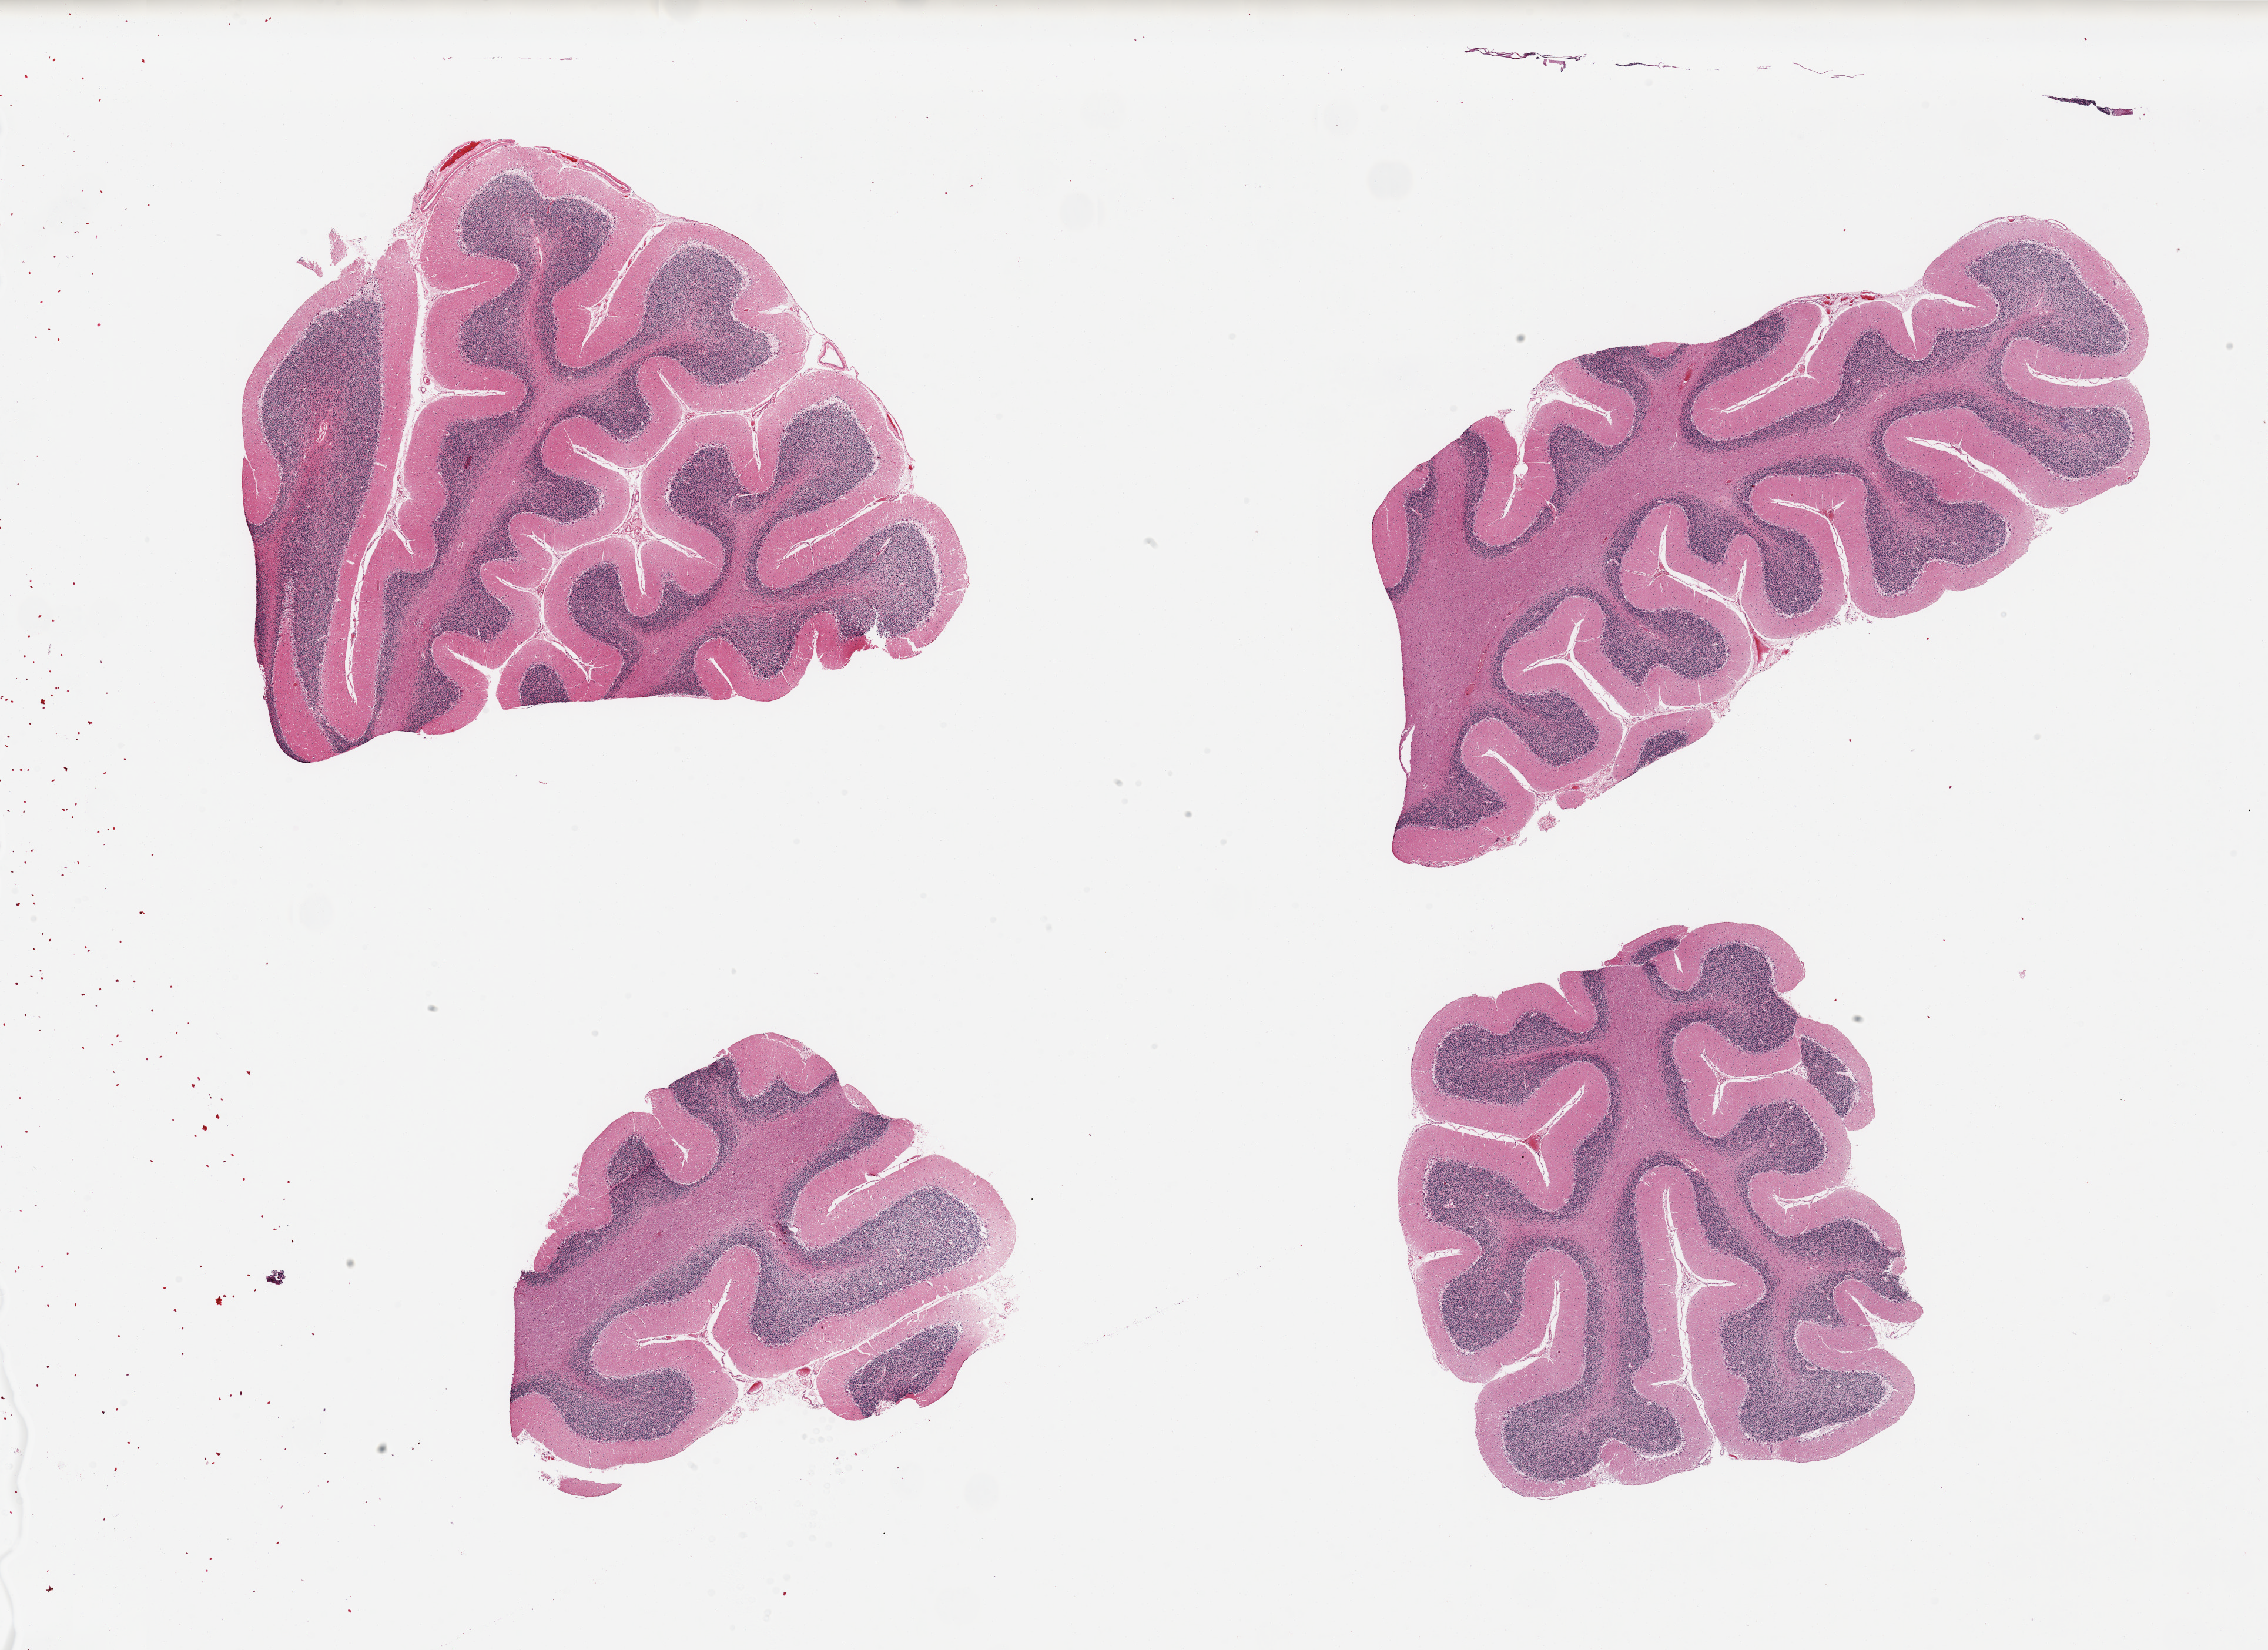
Digitized hematoxylin and eosin (H&E)-stained section, brightfield, whole scanned area (about 30.5 x 22.2 mm, acquisition: 20x scan) shown as a low-resolution overview. PAXgene-fixed paraffin-embedded (PFPE) section. Sampled site (target tissue): cerebellum. Tissue donor sample. Donor: male.
Reviewer comment on this tissue sample: 4 pieces well dissected.